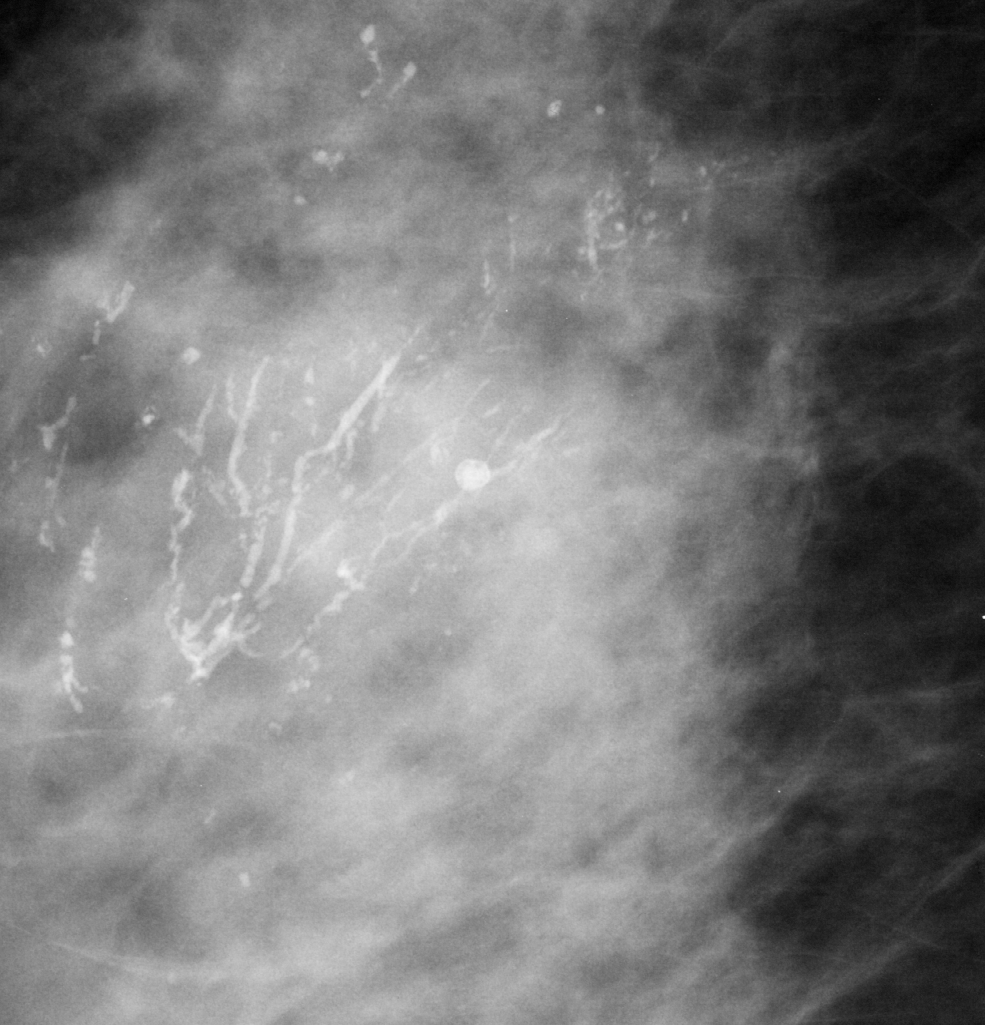
Cropped region of a digitized screen-film mammogram centred on a radiologist-marked abnormality, right breast, MLO view.
- Calcifications, morphology fine linear branching, distribution segmental; BI-RADS assessment category 5; pathology (as recorded): malignant.